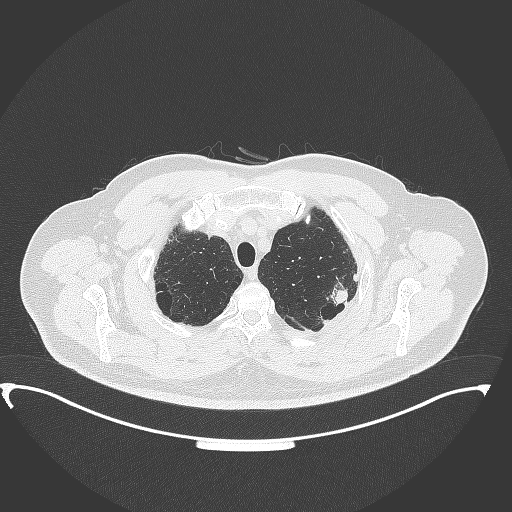
Chest CT, one axial slice; position 315 of 350 along the scan axis; reconstruction kernel B70f; lung window (W 1500 / L -600 HU); 1 mm slice thickness; 512 × 512 image matrix, field of view 459 × 459 mm. Male patient, age 64 years. From the clinical record (not read from this slice): clinical TNM (as recorded): T1c N1 M1.
Outlined on this slice (rectangle marked by the reading radiologist):
- lung tumour (recorded histology: adenocarcinoma): bounding box <328,281,353,311> (left, top, right, bottom; pixels)